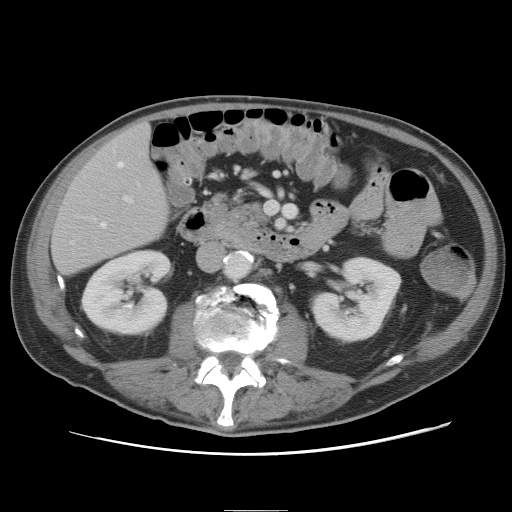
Contrast-enhanced abdominal CT, one axial slice; position 21 of 89 along the scan axis; 120 kVp; intravenous contrast given; soft-tissue window (W 400 / L 40 HU); 5 mm slice thickness; 512 × 512 image matrix, field of view 375 × 375 mm. Male patient, age 69 years. From the clinical record (not read from this slice): diagnosis: colorectal cancer liver metastases, imaged before liver resection; multiple liver metastases: no; largest metastasis: 8.5 cm; disease in both lobes: no.
Annotated regions visible in this slice (manually delineated by an expert):
- hepatic veins: bounding box <72,162,124,243> (left, top, right, bottom; pixels)
- liver: <52,124,169,274>
- planned liver remnant (the part of the liver to remain after resection): <53,124,169,274>
- portal vein (with intrahepatic branches): <123,196,132,202>